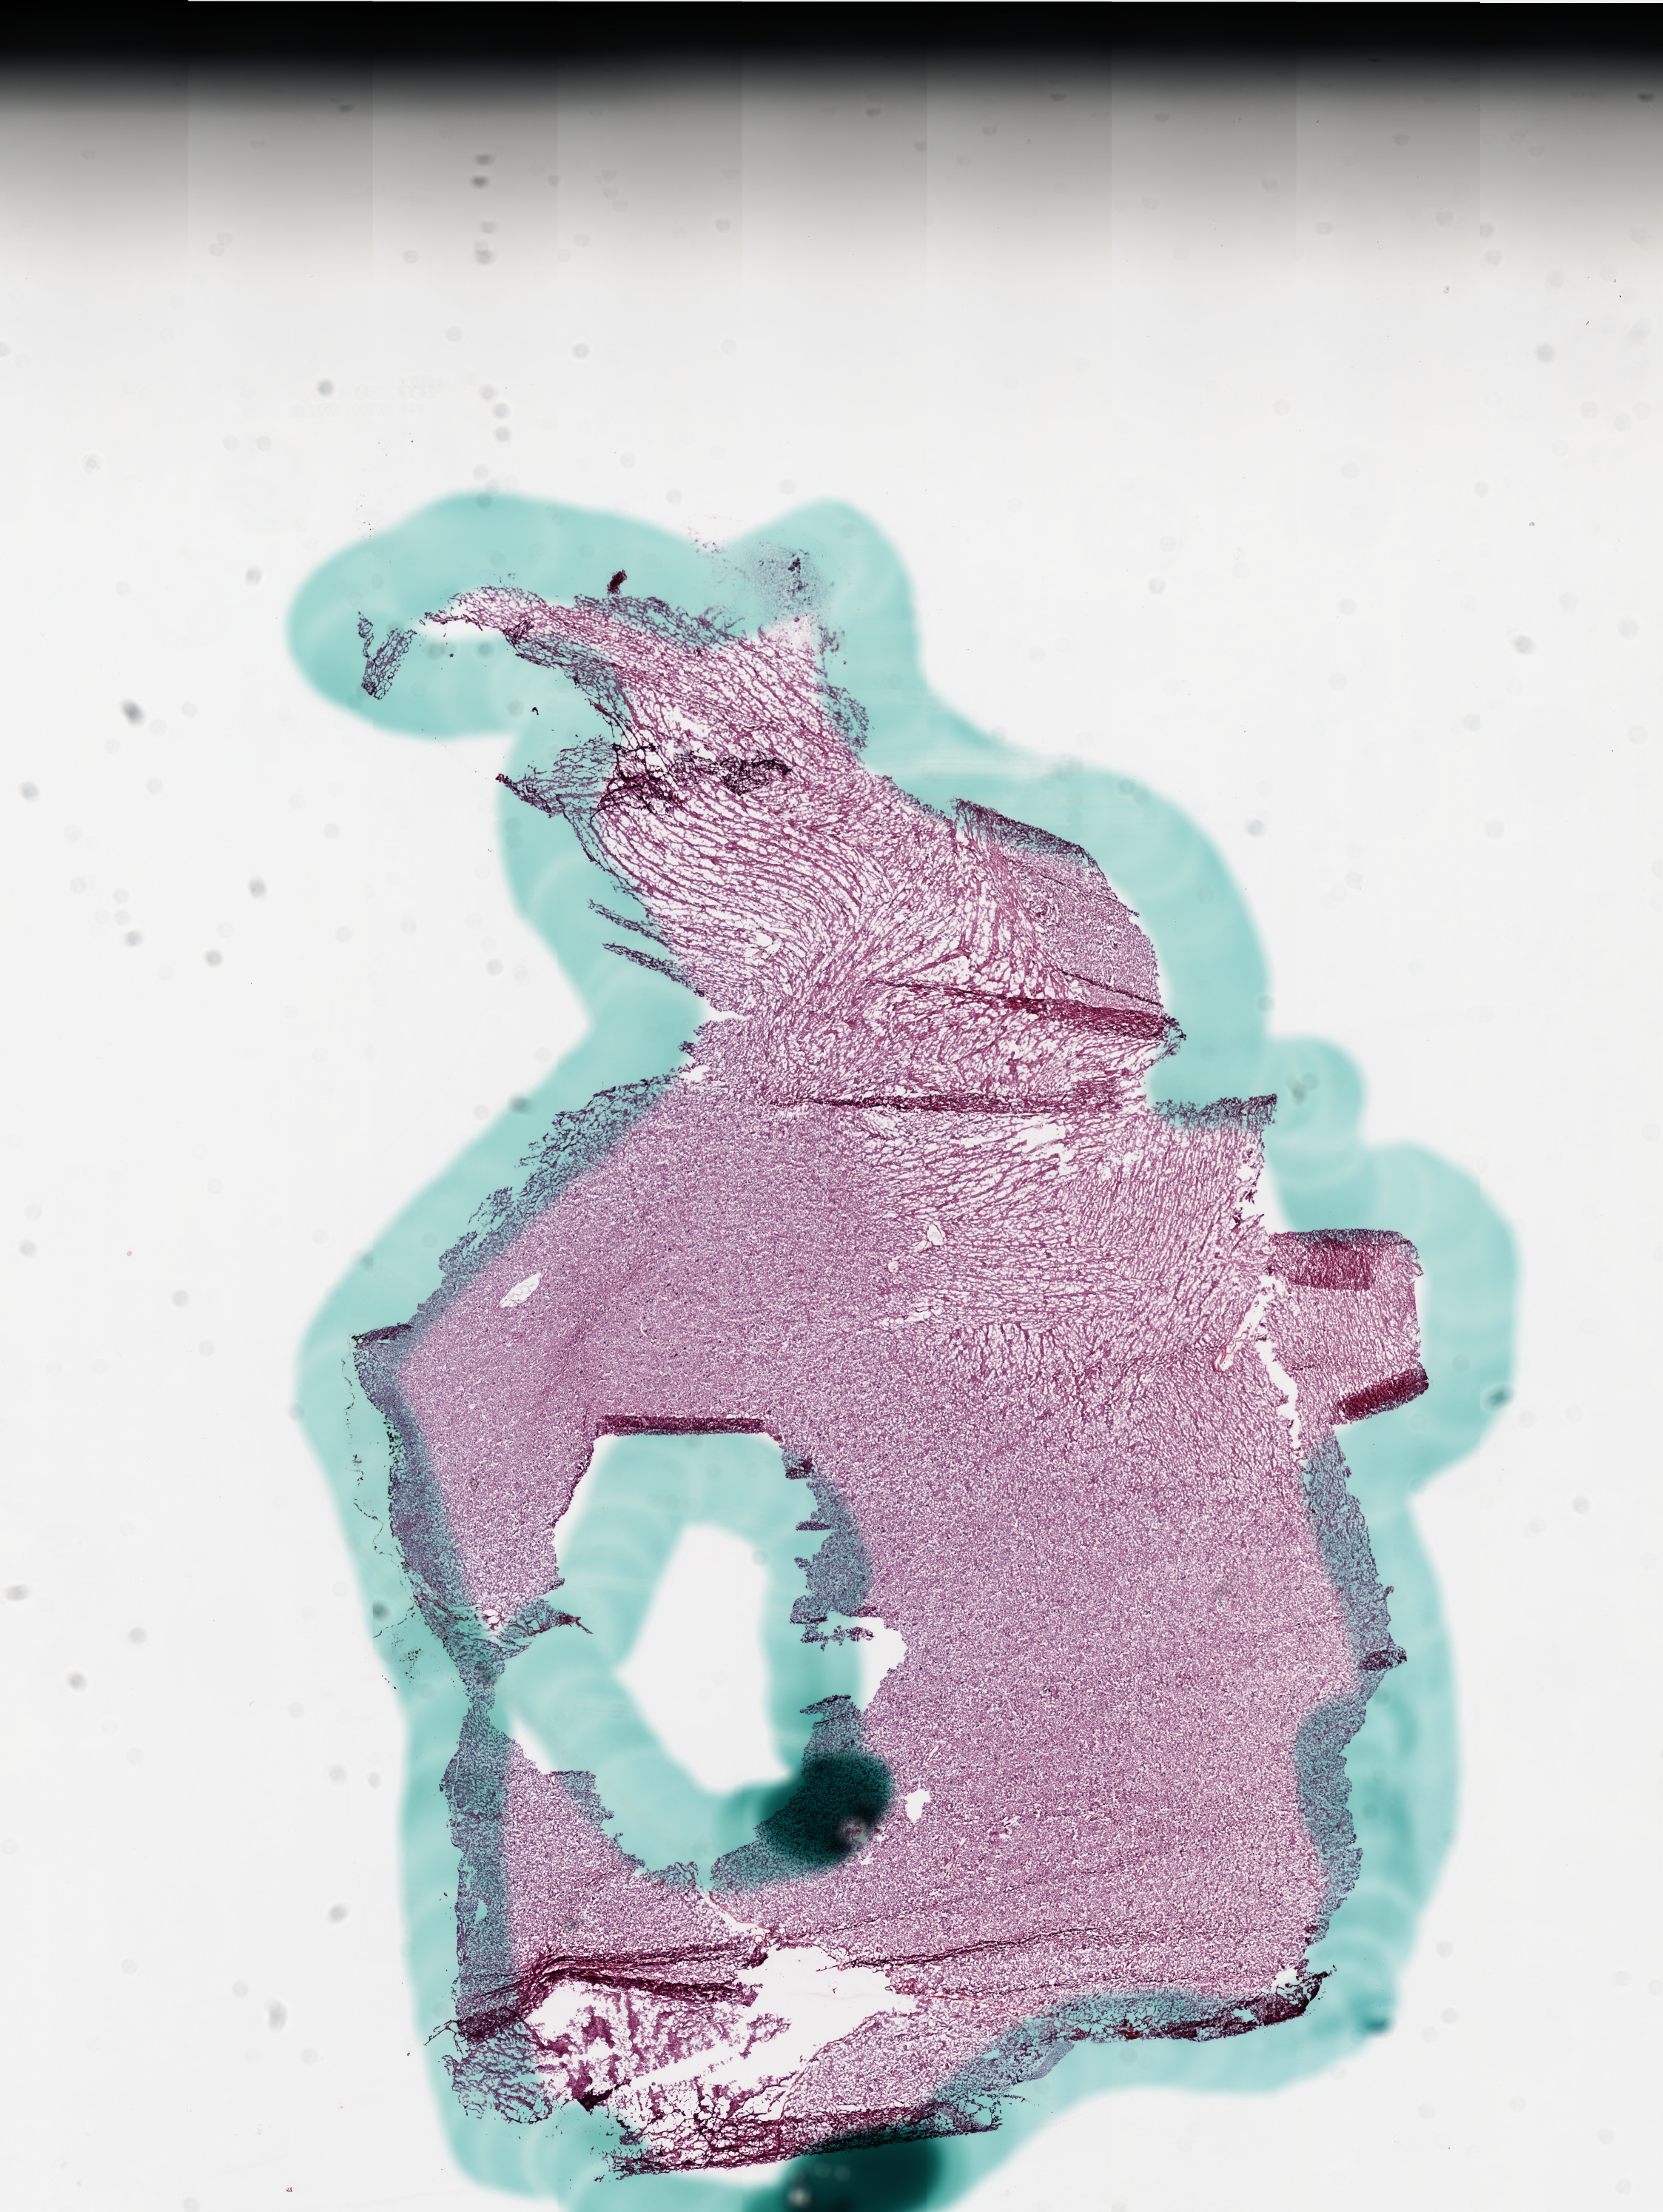
Whole-slide histology image, H&E-stained, a low-resolution overview of the entire scanned area, about 9.0 x 12.0 mm, frozen section from the bottom of the tissue portion, primary tumour sample from the brain. Female, age 56 years at initial diagnosis. Slide review estimates, as recorded: tumour cells 0%, tumour nuclei 0%, normal cells 100%, stromal cells 0%, necrosis 0%.
Histologic diagnosis: Glioblastoma.